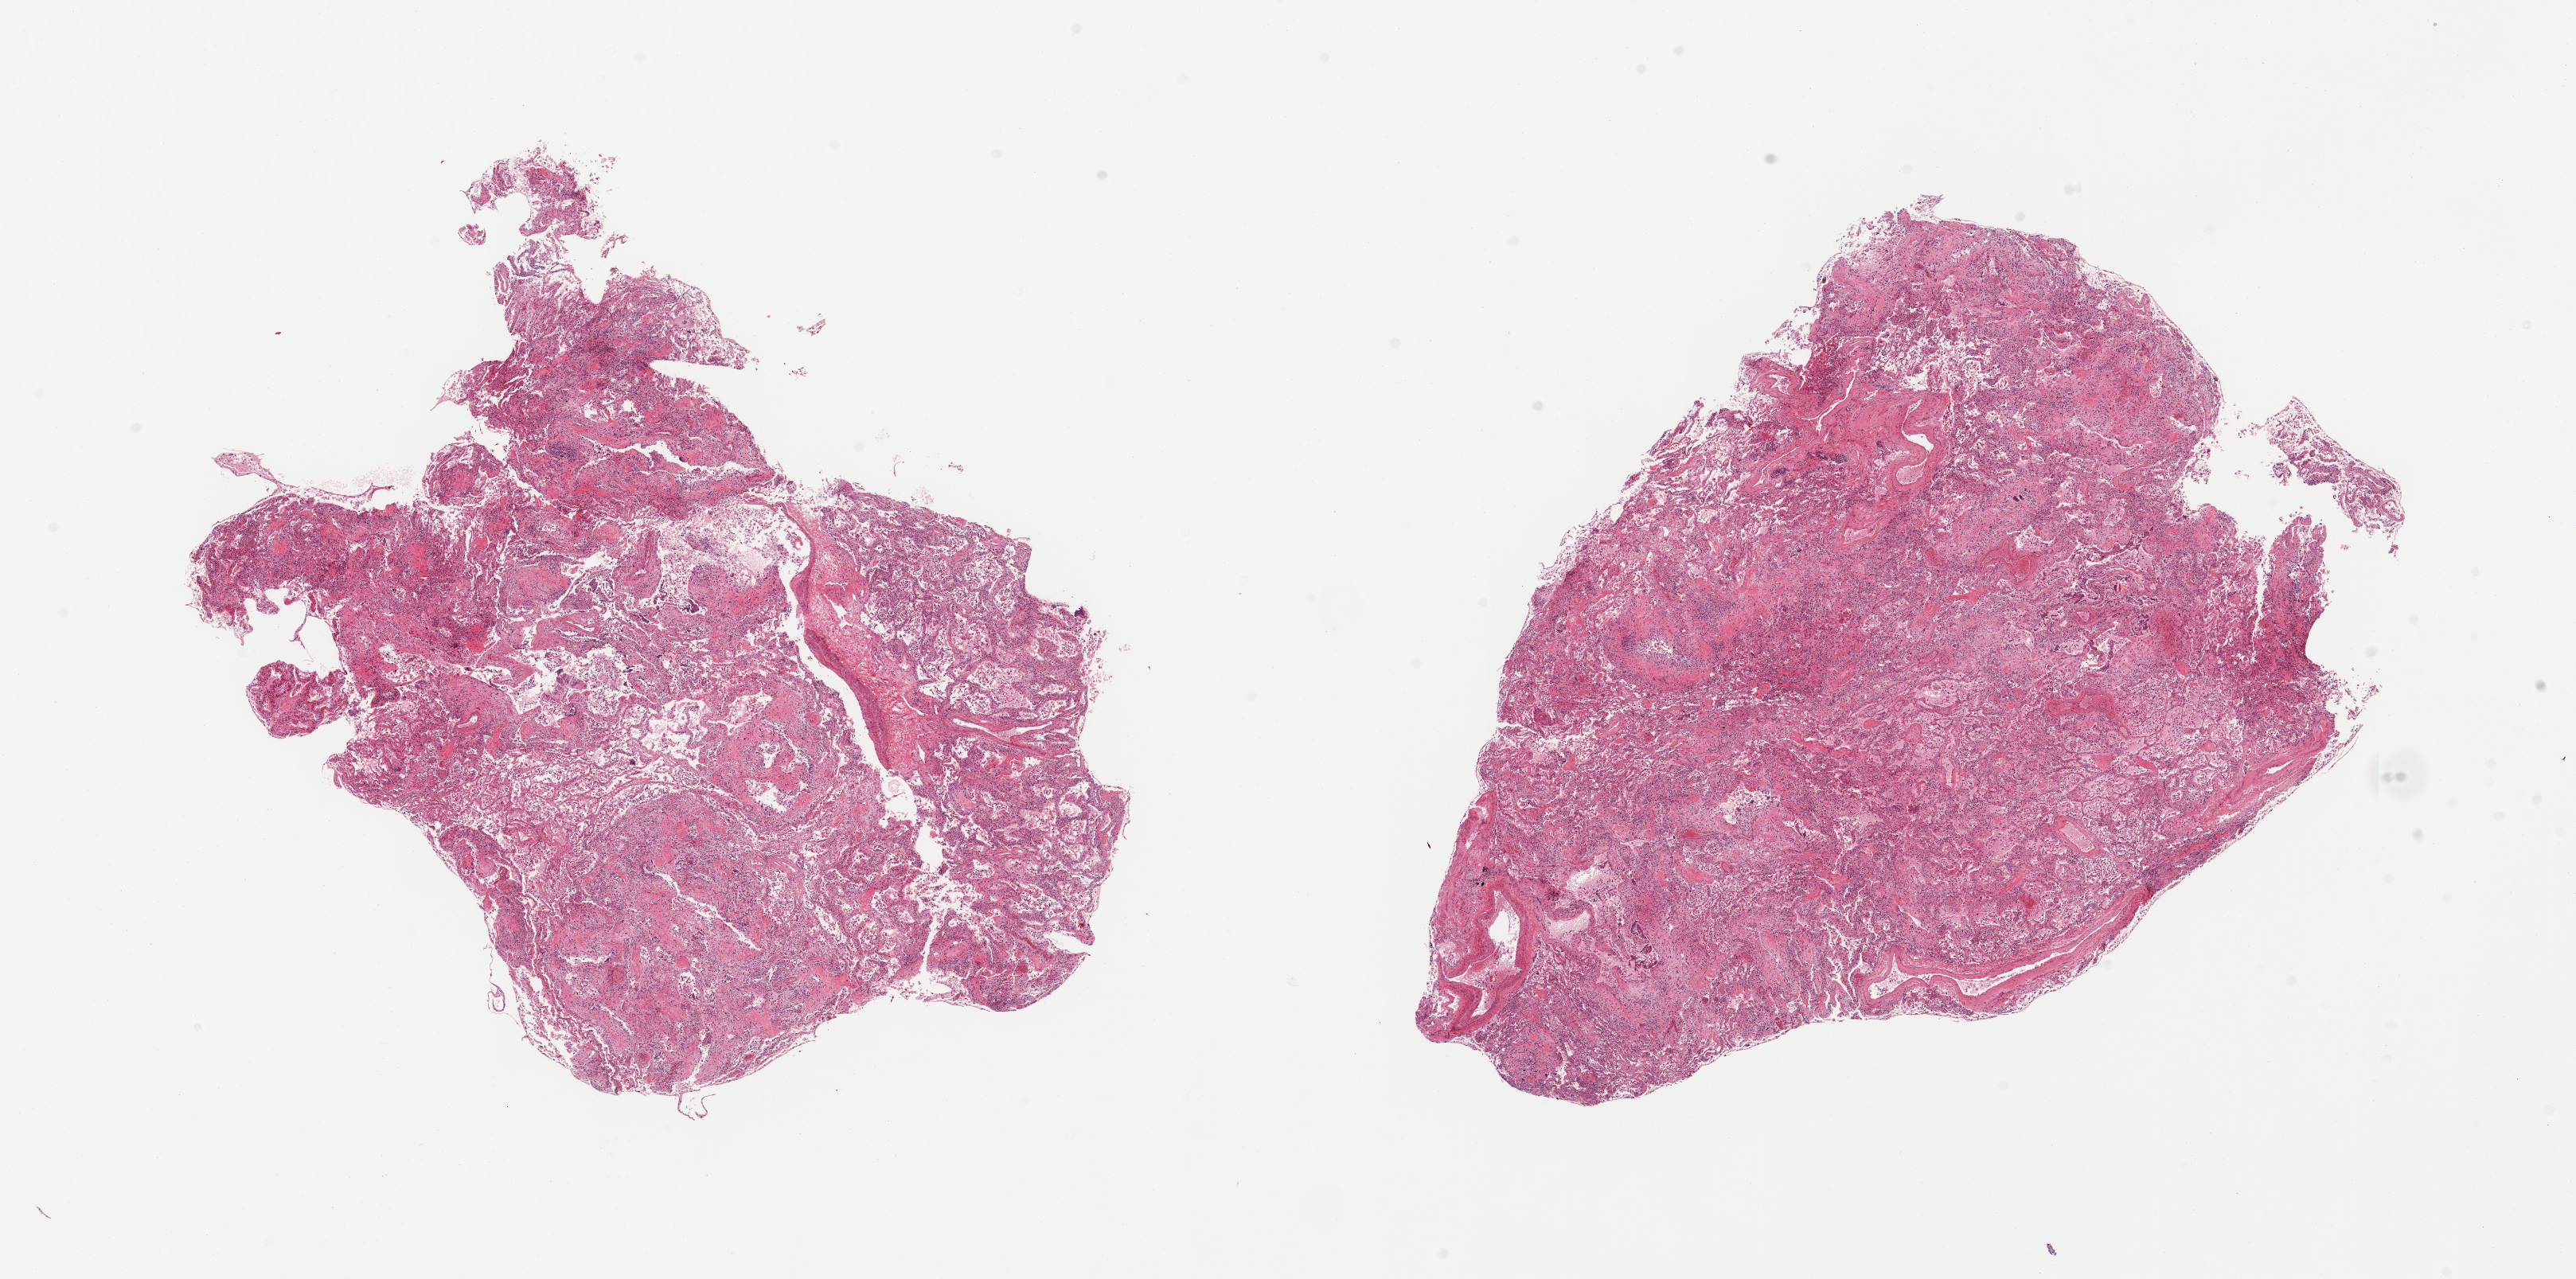
Whole-slide image, haematoxylin and eosin stain — shown as a low-resolution overview of the whole scanned area (about 25.6 x 12.7 mm, acquisition: 20x scan); PAXgene-fixed, paraffin-embedded tissue; section of lung (target tissue); donor tissue sample. Donor: male.
- review note (as recorded): 2 pieces; changes compatible with ARDS